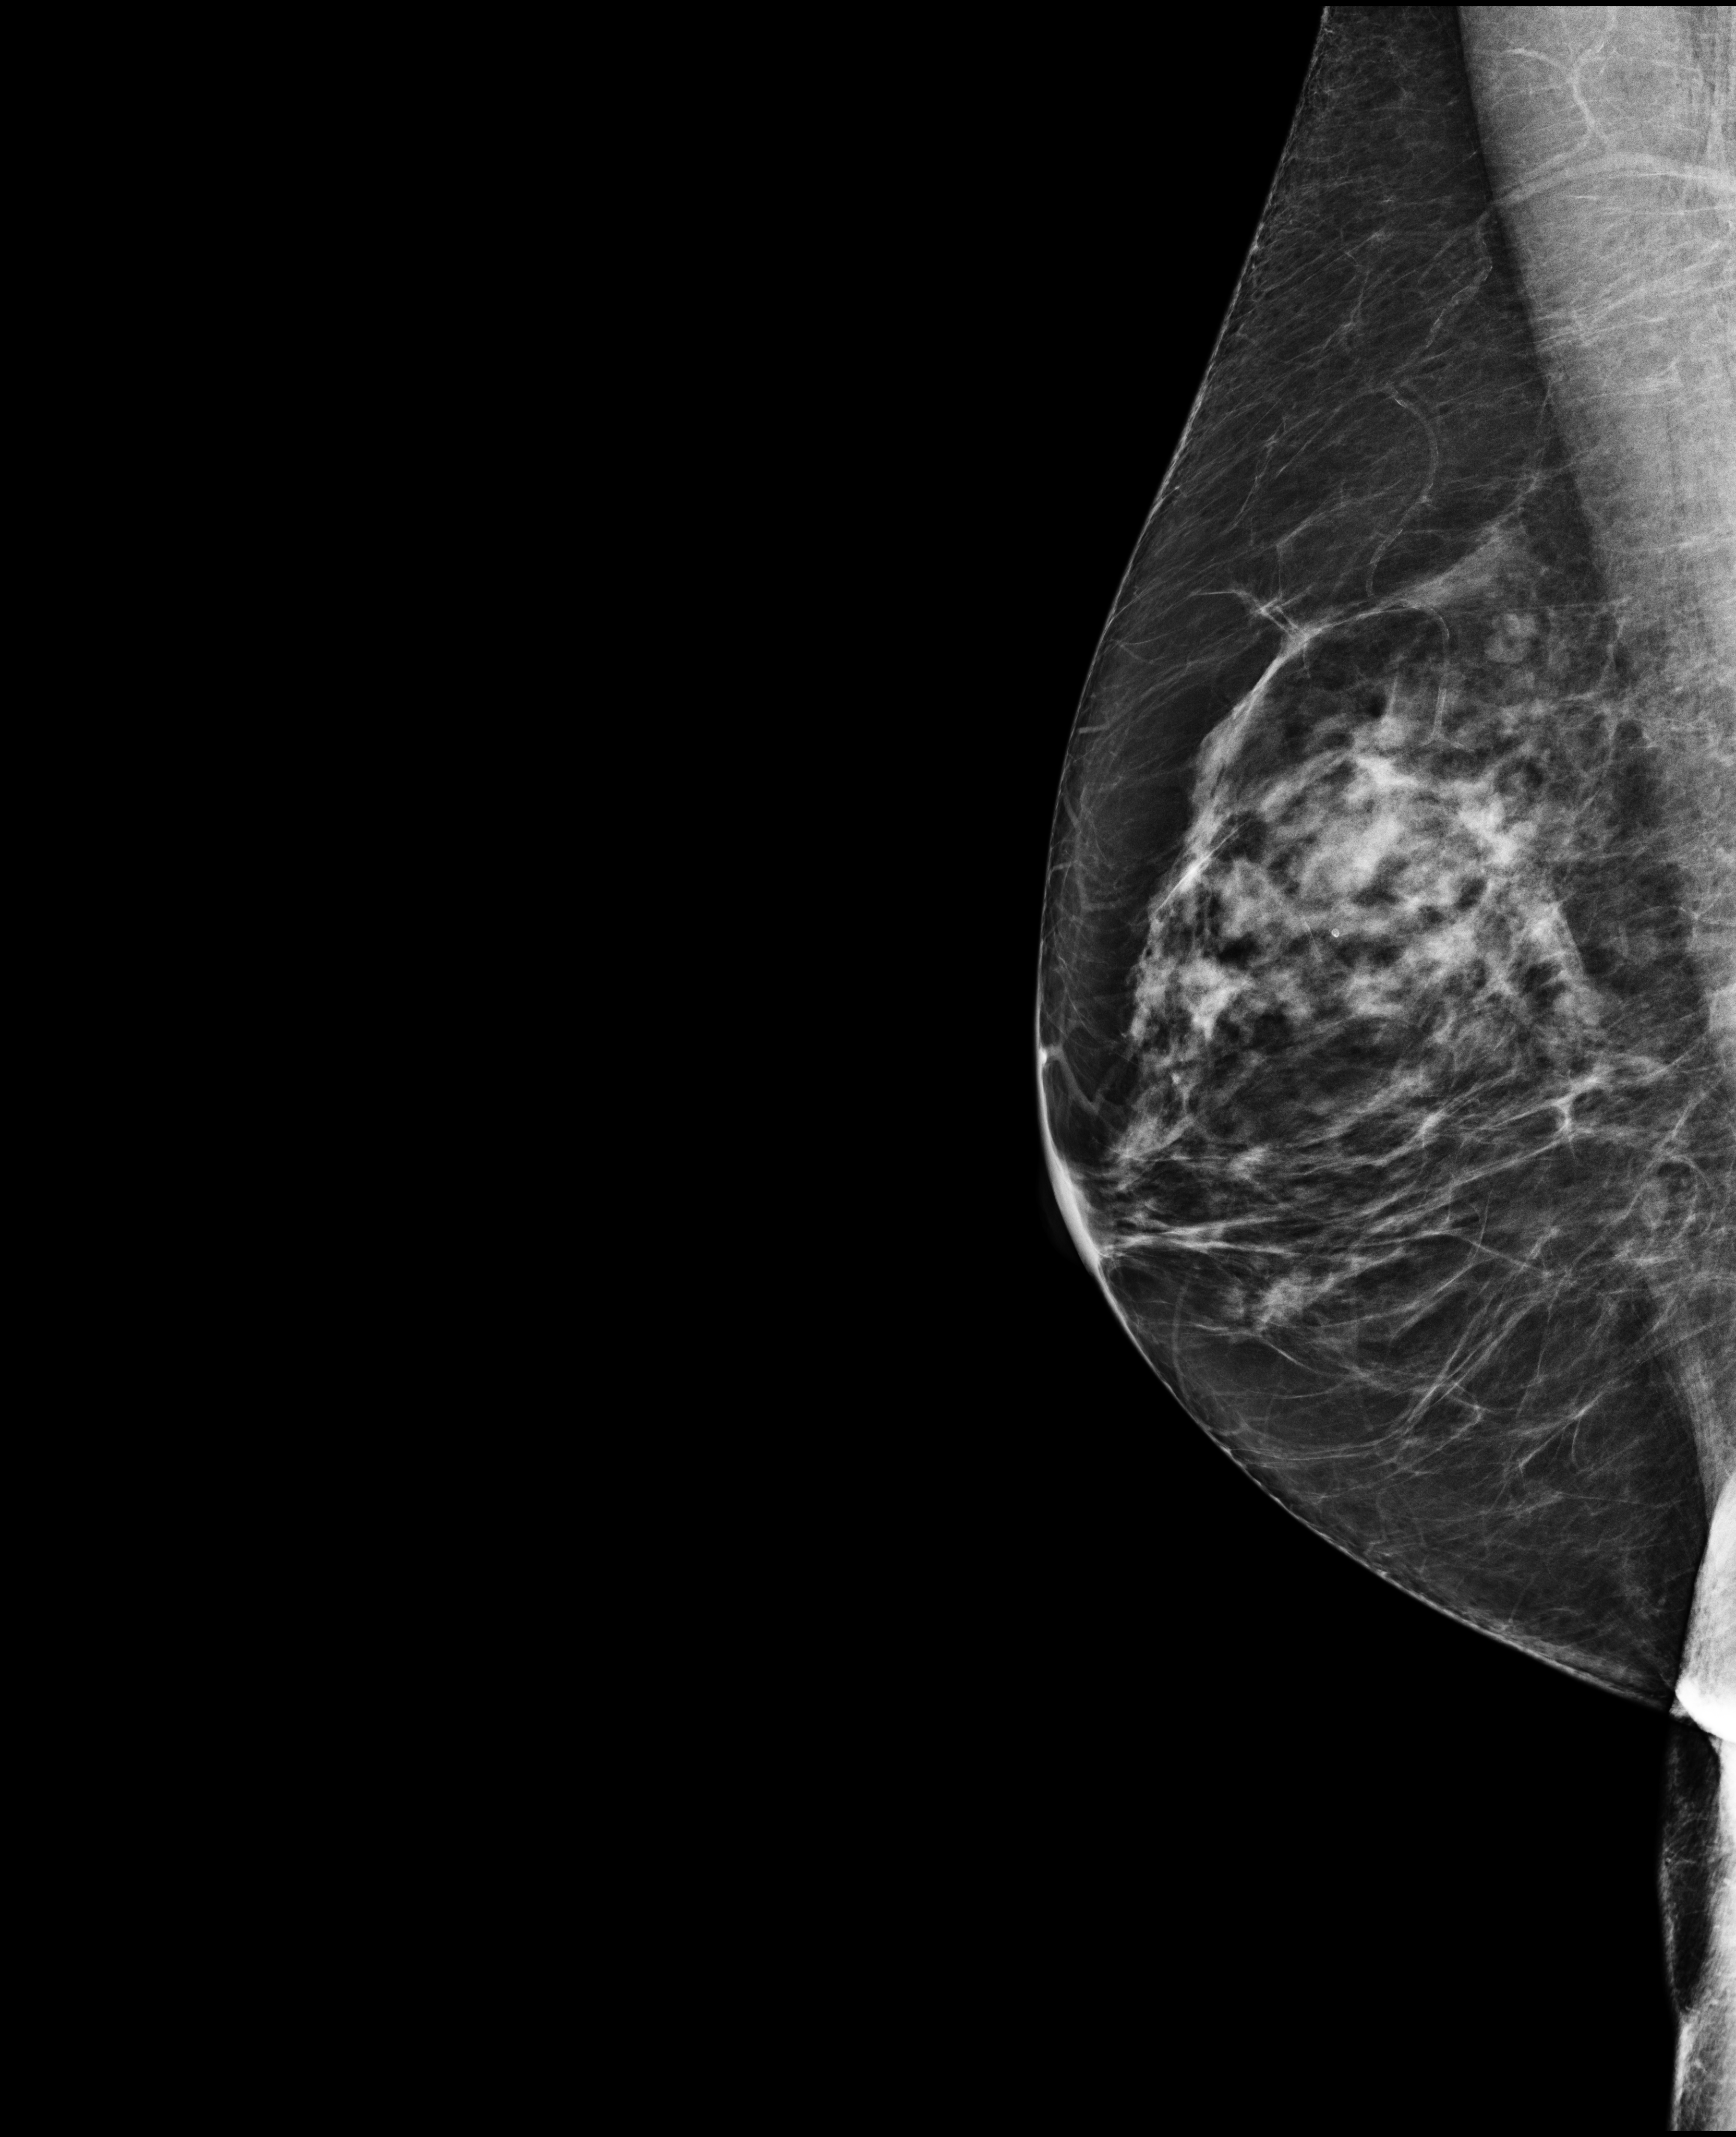
Screening examination, compressed breast thickness 69 mm. Patient aged 68 years (female).
Image type: full-field digital mammogram. Breast: right. Projection: medio-lateral oblique projection.